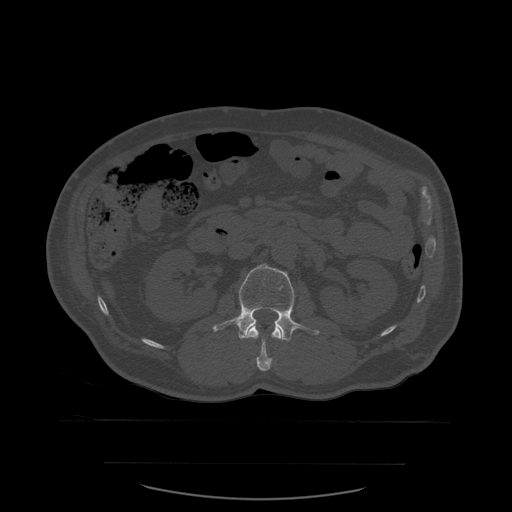
CT including the spine, one axial slice; slice 228 of 590 in the series (ordered by position); bone window (W 1800 / L 400 HU); 512 × 512 image matrix, field of view 479 × 479 mm. Patient age 71 years. From the clinical record (not read from this slice): primary cancer: lung; vertebrae with lytic lesions (as recorded): T1, T2, L5, S1.
Structures marked on this image (semi-automatic segmentation, software-assisted and operator-edited):
- L1 vertebra: bounding box [x1, y1, x2, y2] px = [247, 326, 282, 372]
- L2 vertebra: [213, 264, 320, 342]